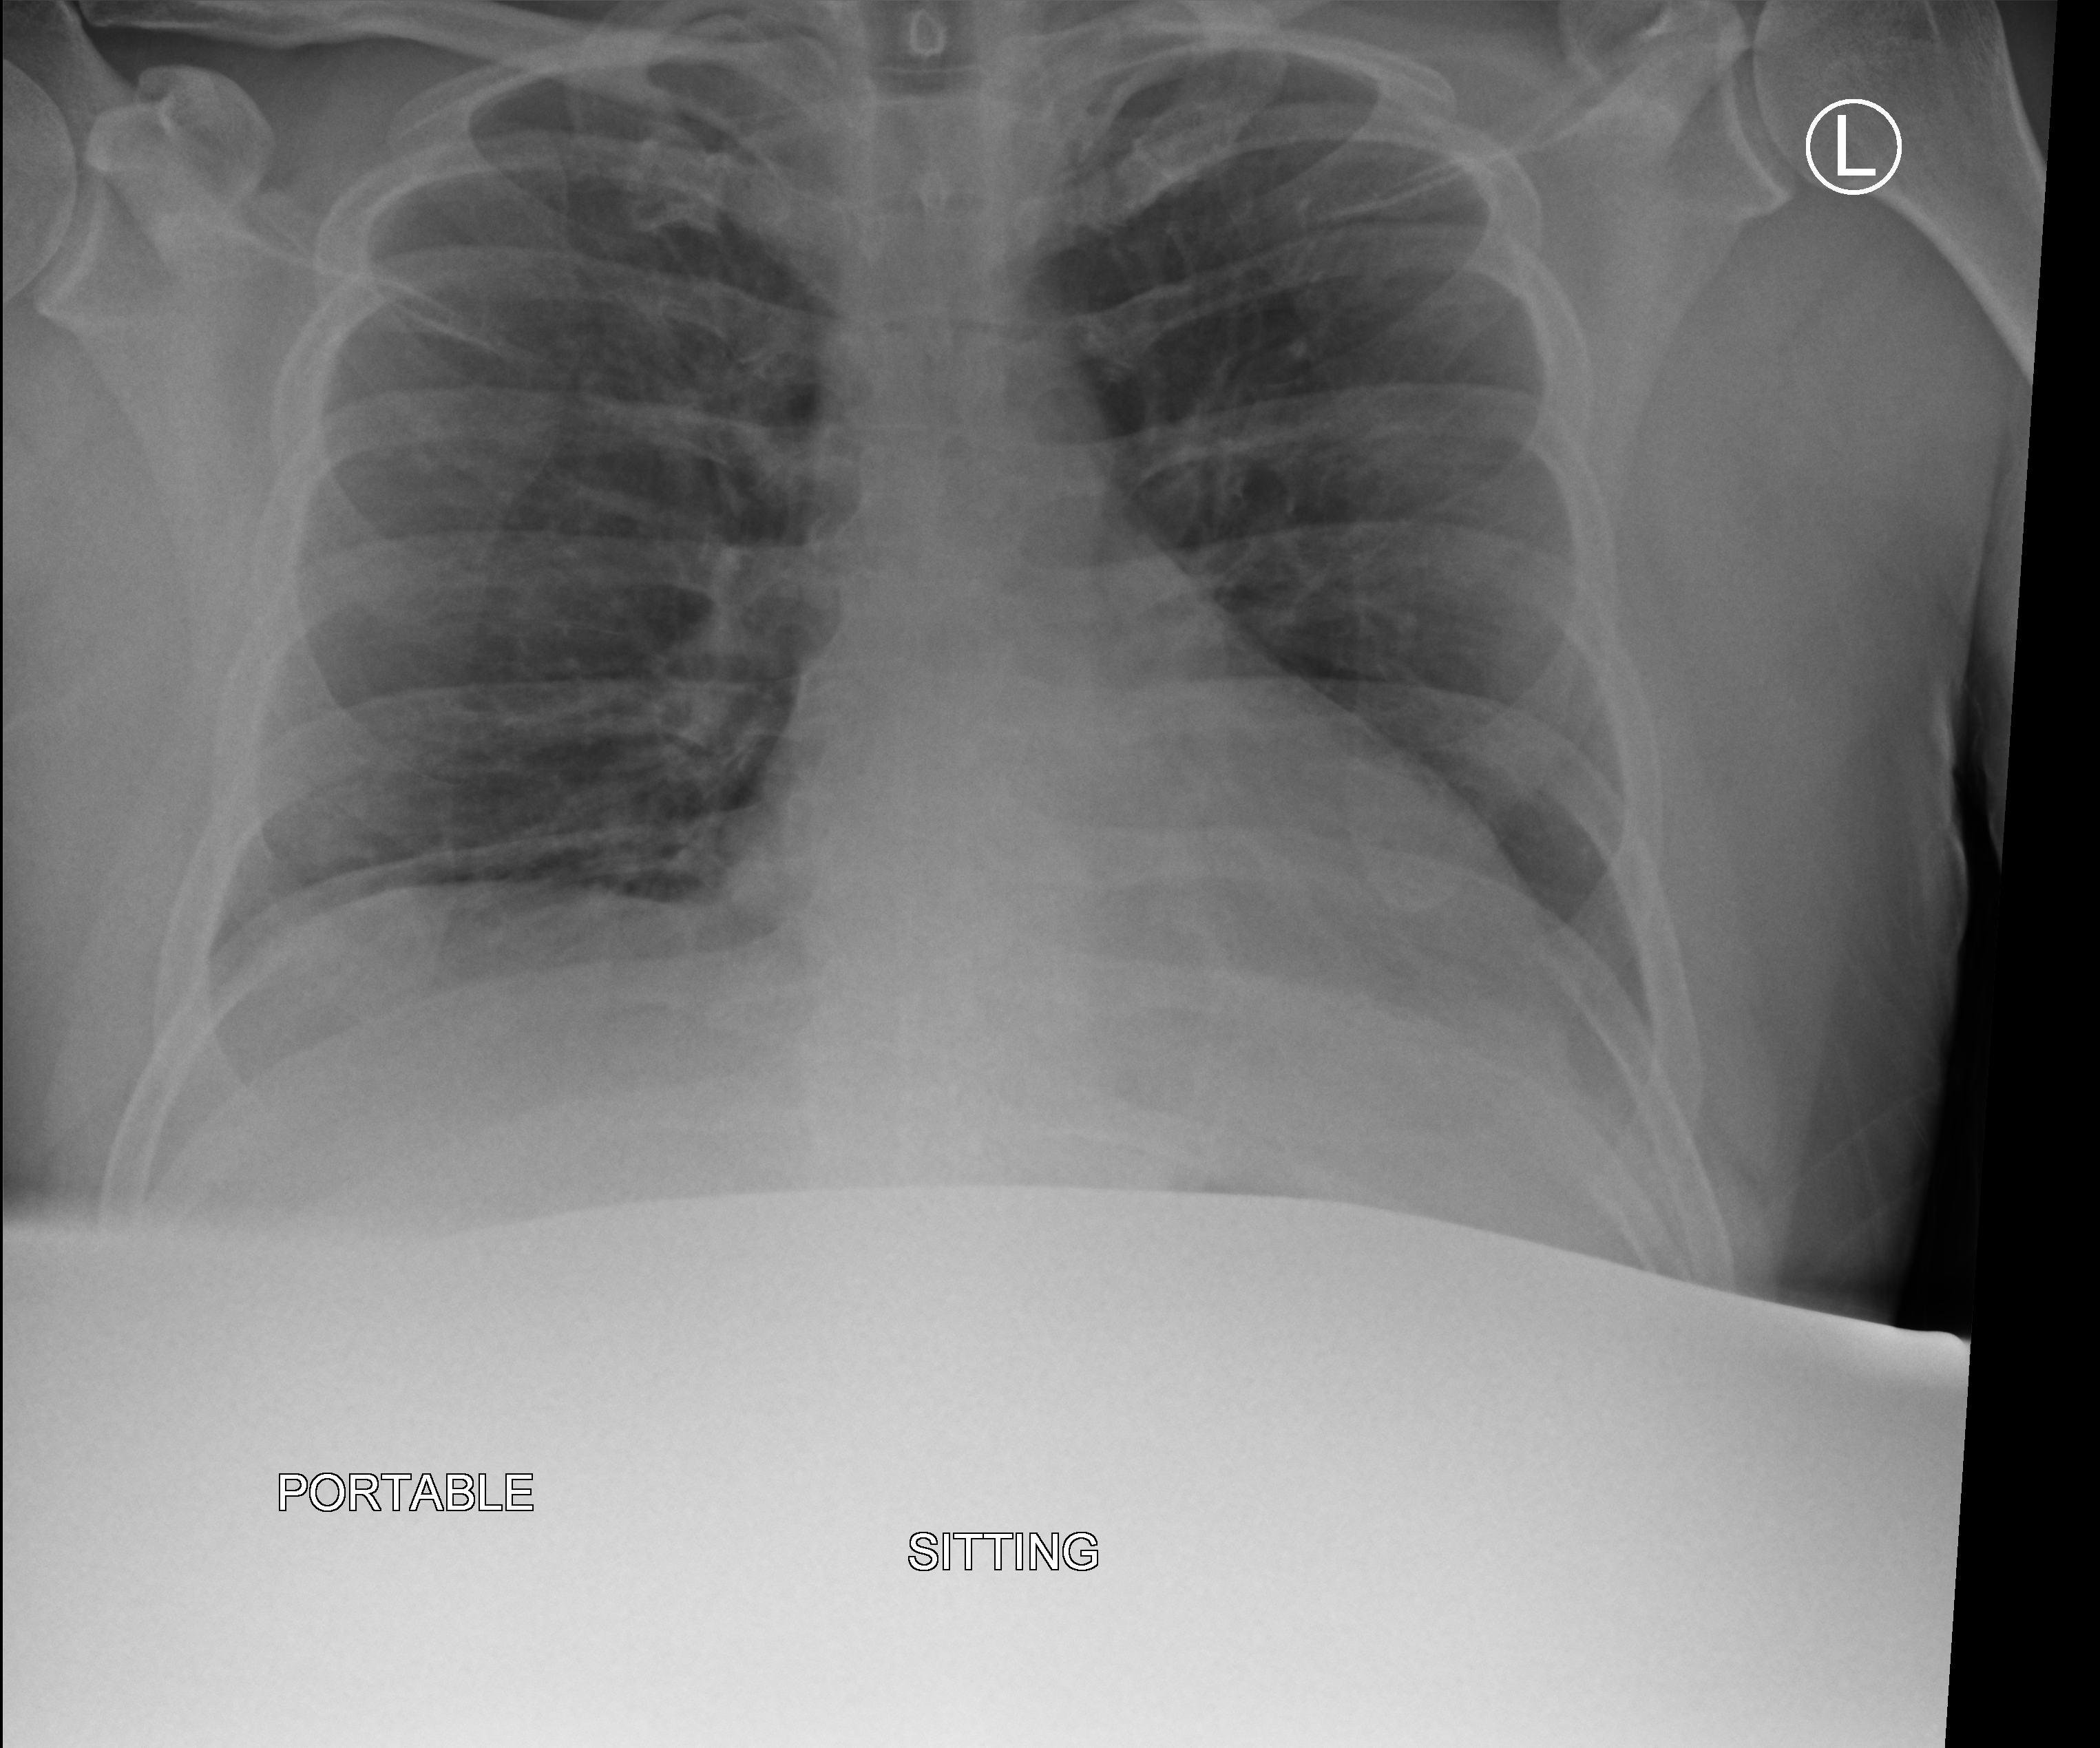
Bedside chest radiograph (computed radiography); anteroposterior (AP) projection. Patient hospitalised with COVID-19; male, aged 18–59 years.
From the hospital-stay record, not from the radiograph (when in the stay this image was taken is not recorded):
- hypertension (admission record): yes